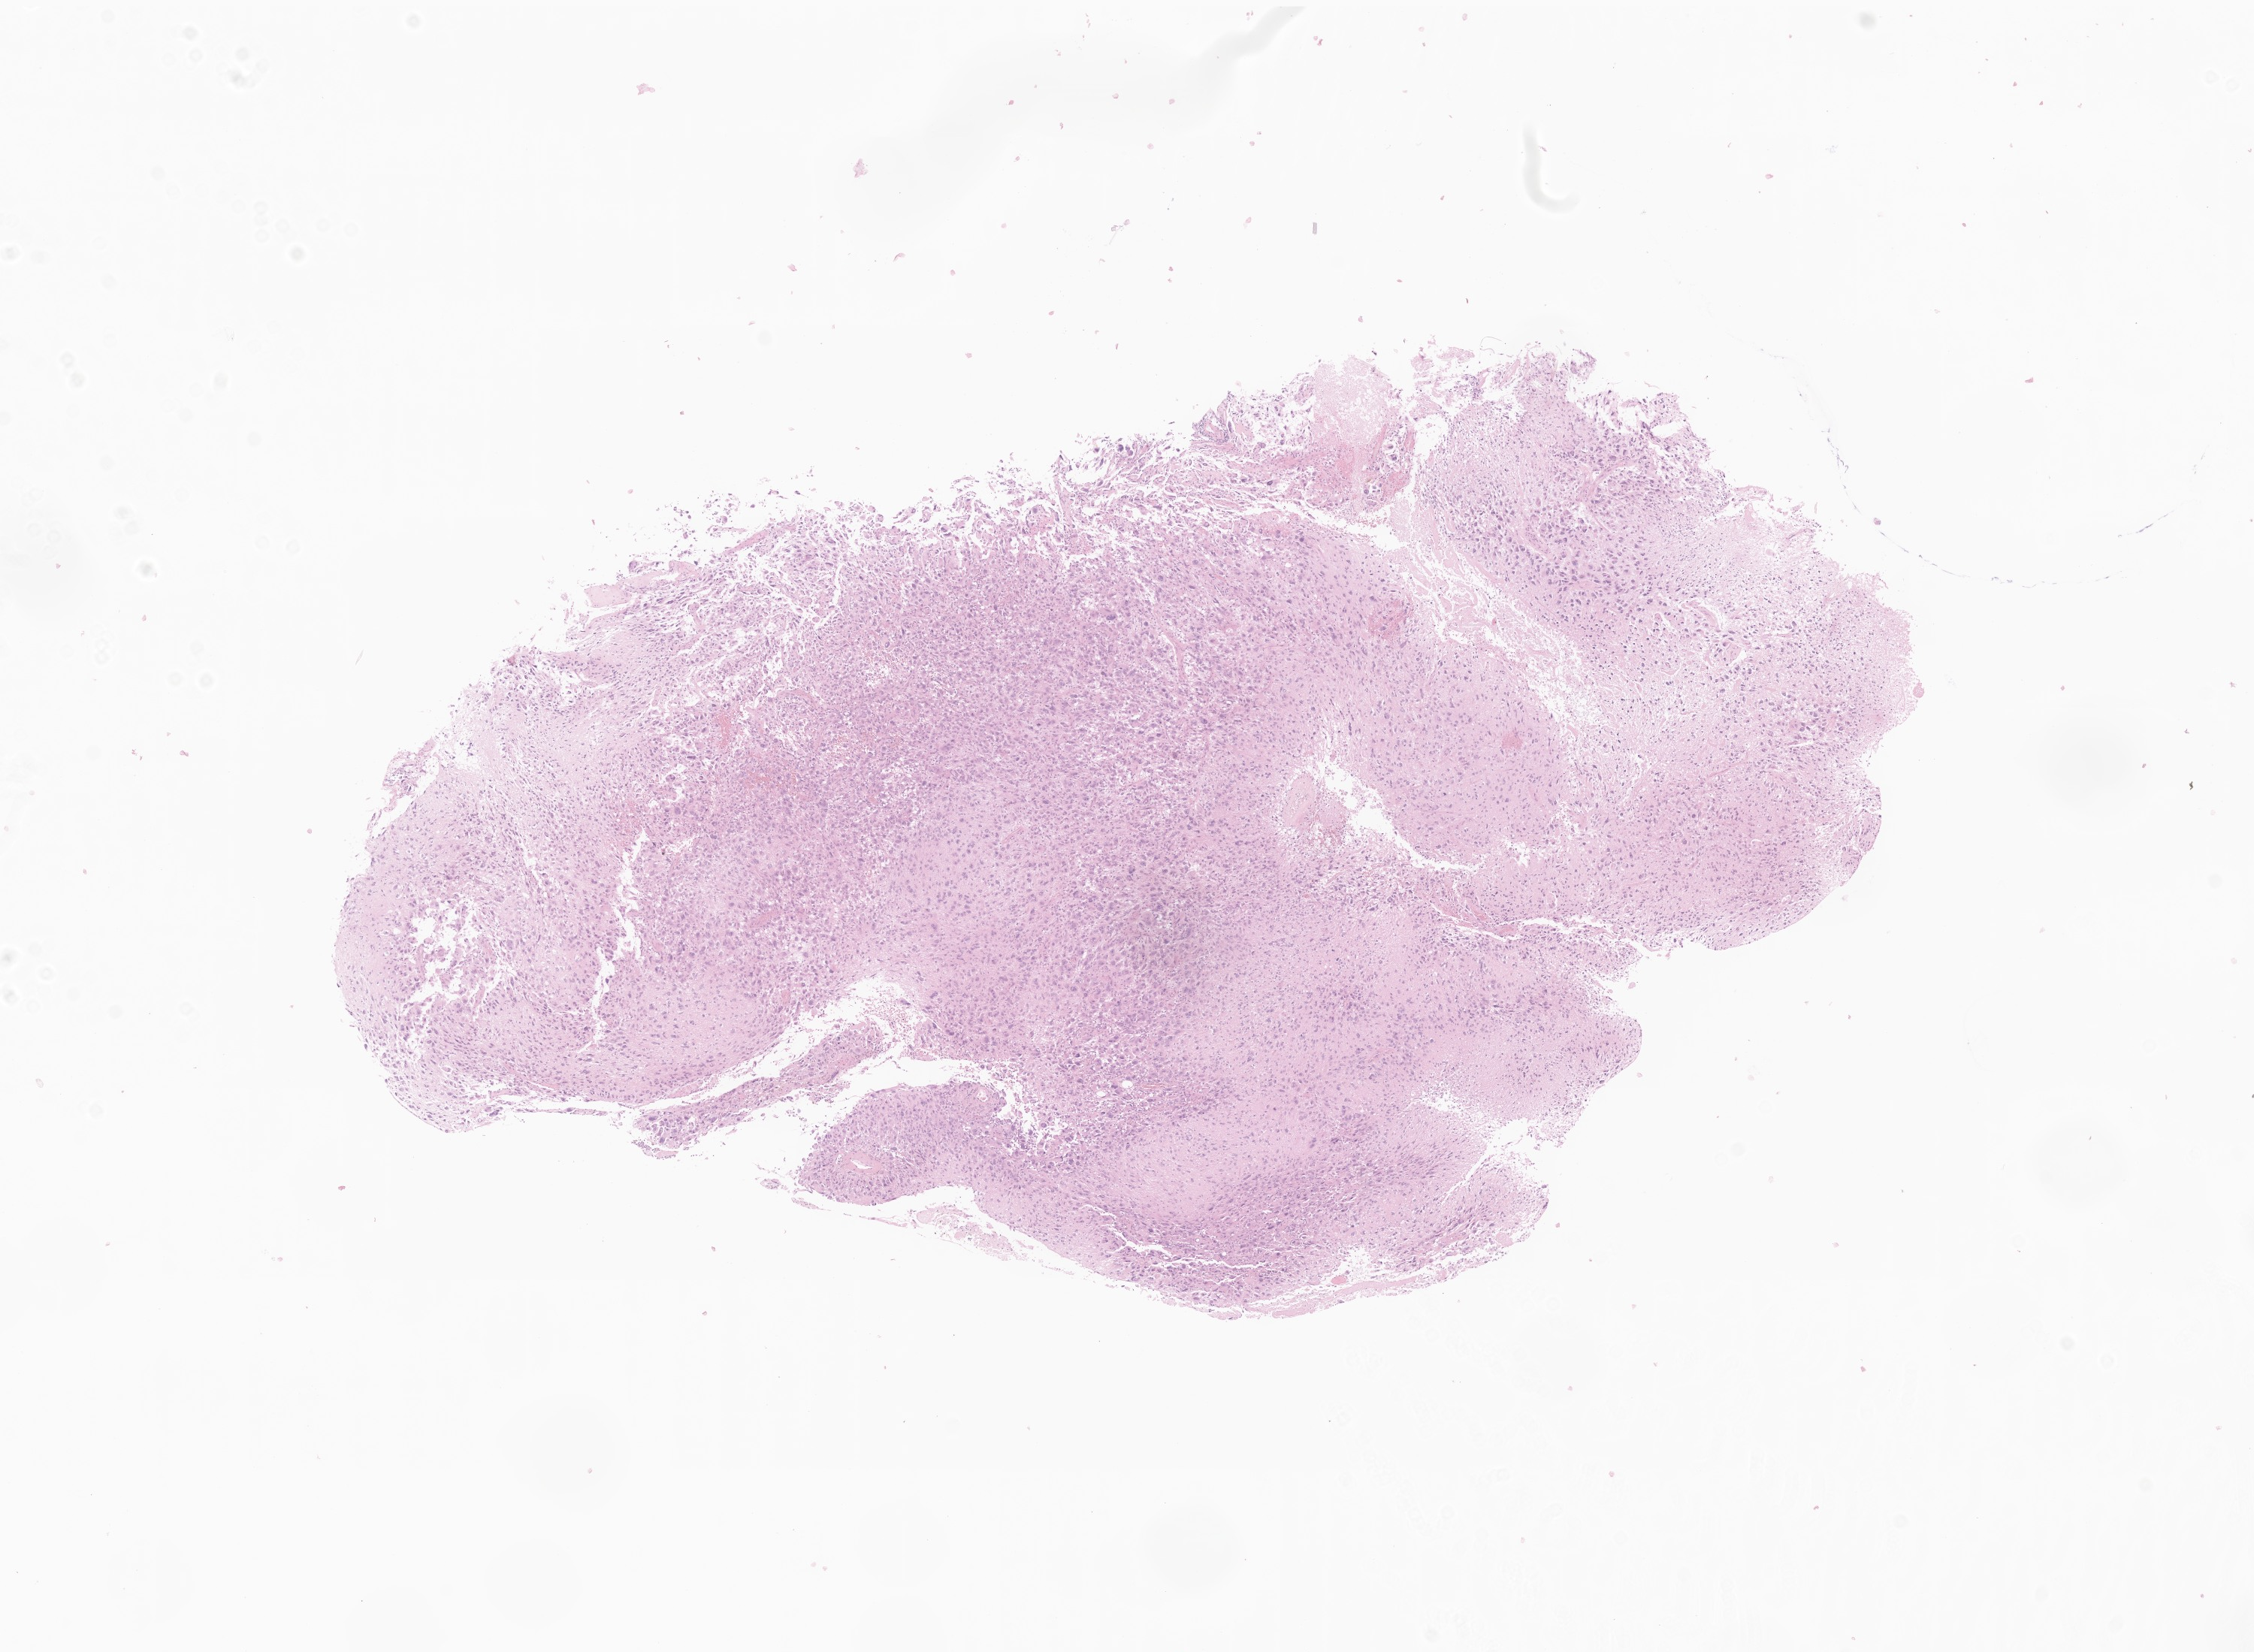
H&E whole-slide image — whole scanned area (about 12.6 x 9.3 mm) shown as a low-resolution overview. Formalin-fixed paraffin-embedded section. Specimen: recurrent tumor. Site: brain. Patient: female, age at initial diagnosis 53 years. Slide review estimates, as recorded: tumor cells 82%, tumor nuclei 90%, stromal cells 10%, necrosis 8%, normal cells 0%. Infiltration values recorded for this section: lymphocyte infiltration 6%, monocyte infiltration 2%, neutrophil infiltration 0%.
Patient diagnosis: Glioblastoma, NOS. Section: bottom of the tissue portion.